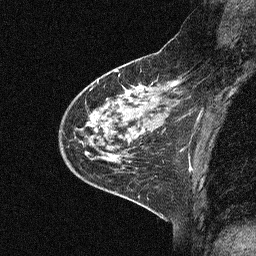
Breast MRI (dynamic contrast-enhanced), one sagittal slice; slice 20 of 64 in the series (ordered by position); dynamic contrast-enhanced study with each time point stored as its own series, time point 2 of 3 at this slice position (early post-contrast, ordered by acquisition time); 1.5 T; TE 4.5 ms, TR 11 ms; 2.06 mm slice thickness; 256 × 256 image matrix, field of view 200 × 200 mm. Patient: female, 46 years. Case-level facts recorded for this patient, not image findings: setting: breast cancer imaged before/during neoadjuvant chemotherapy; receptor status: HER2-positive.
Outlined on this slice (semi-automatically segmented with operator editing):
- analysis volume of interest (the breast-tissue region the enhancement analysis was run in; not a lesion): bounding box [x1, y1, x2, y2] px = [47, 51, 180, 169]
- tumour enhancement mask (voxels above the 90 % enhancement threshold inside the analysis volume of interest): [89, 90, 126, 120]